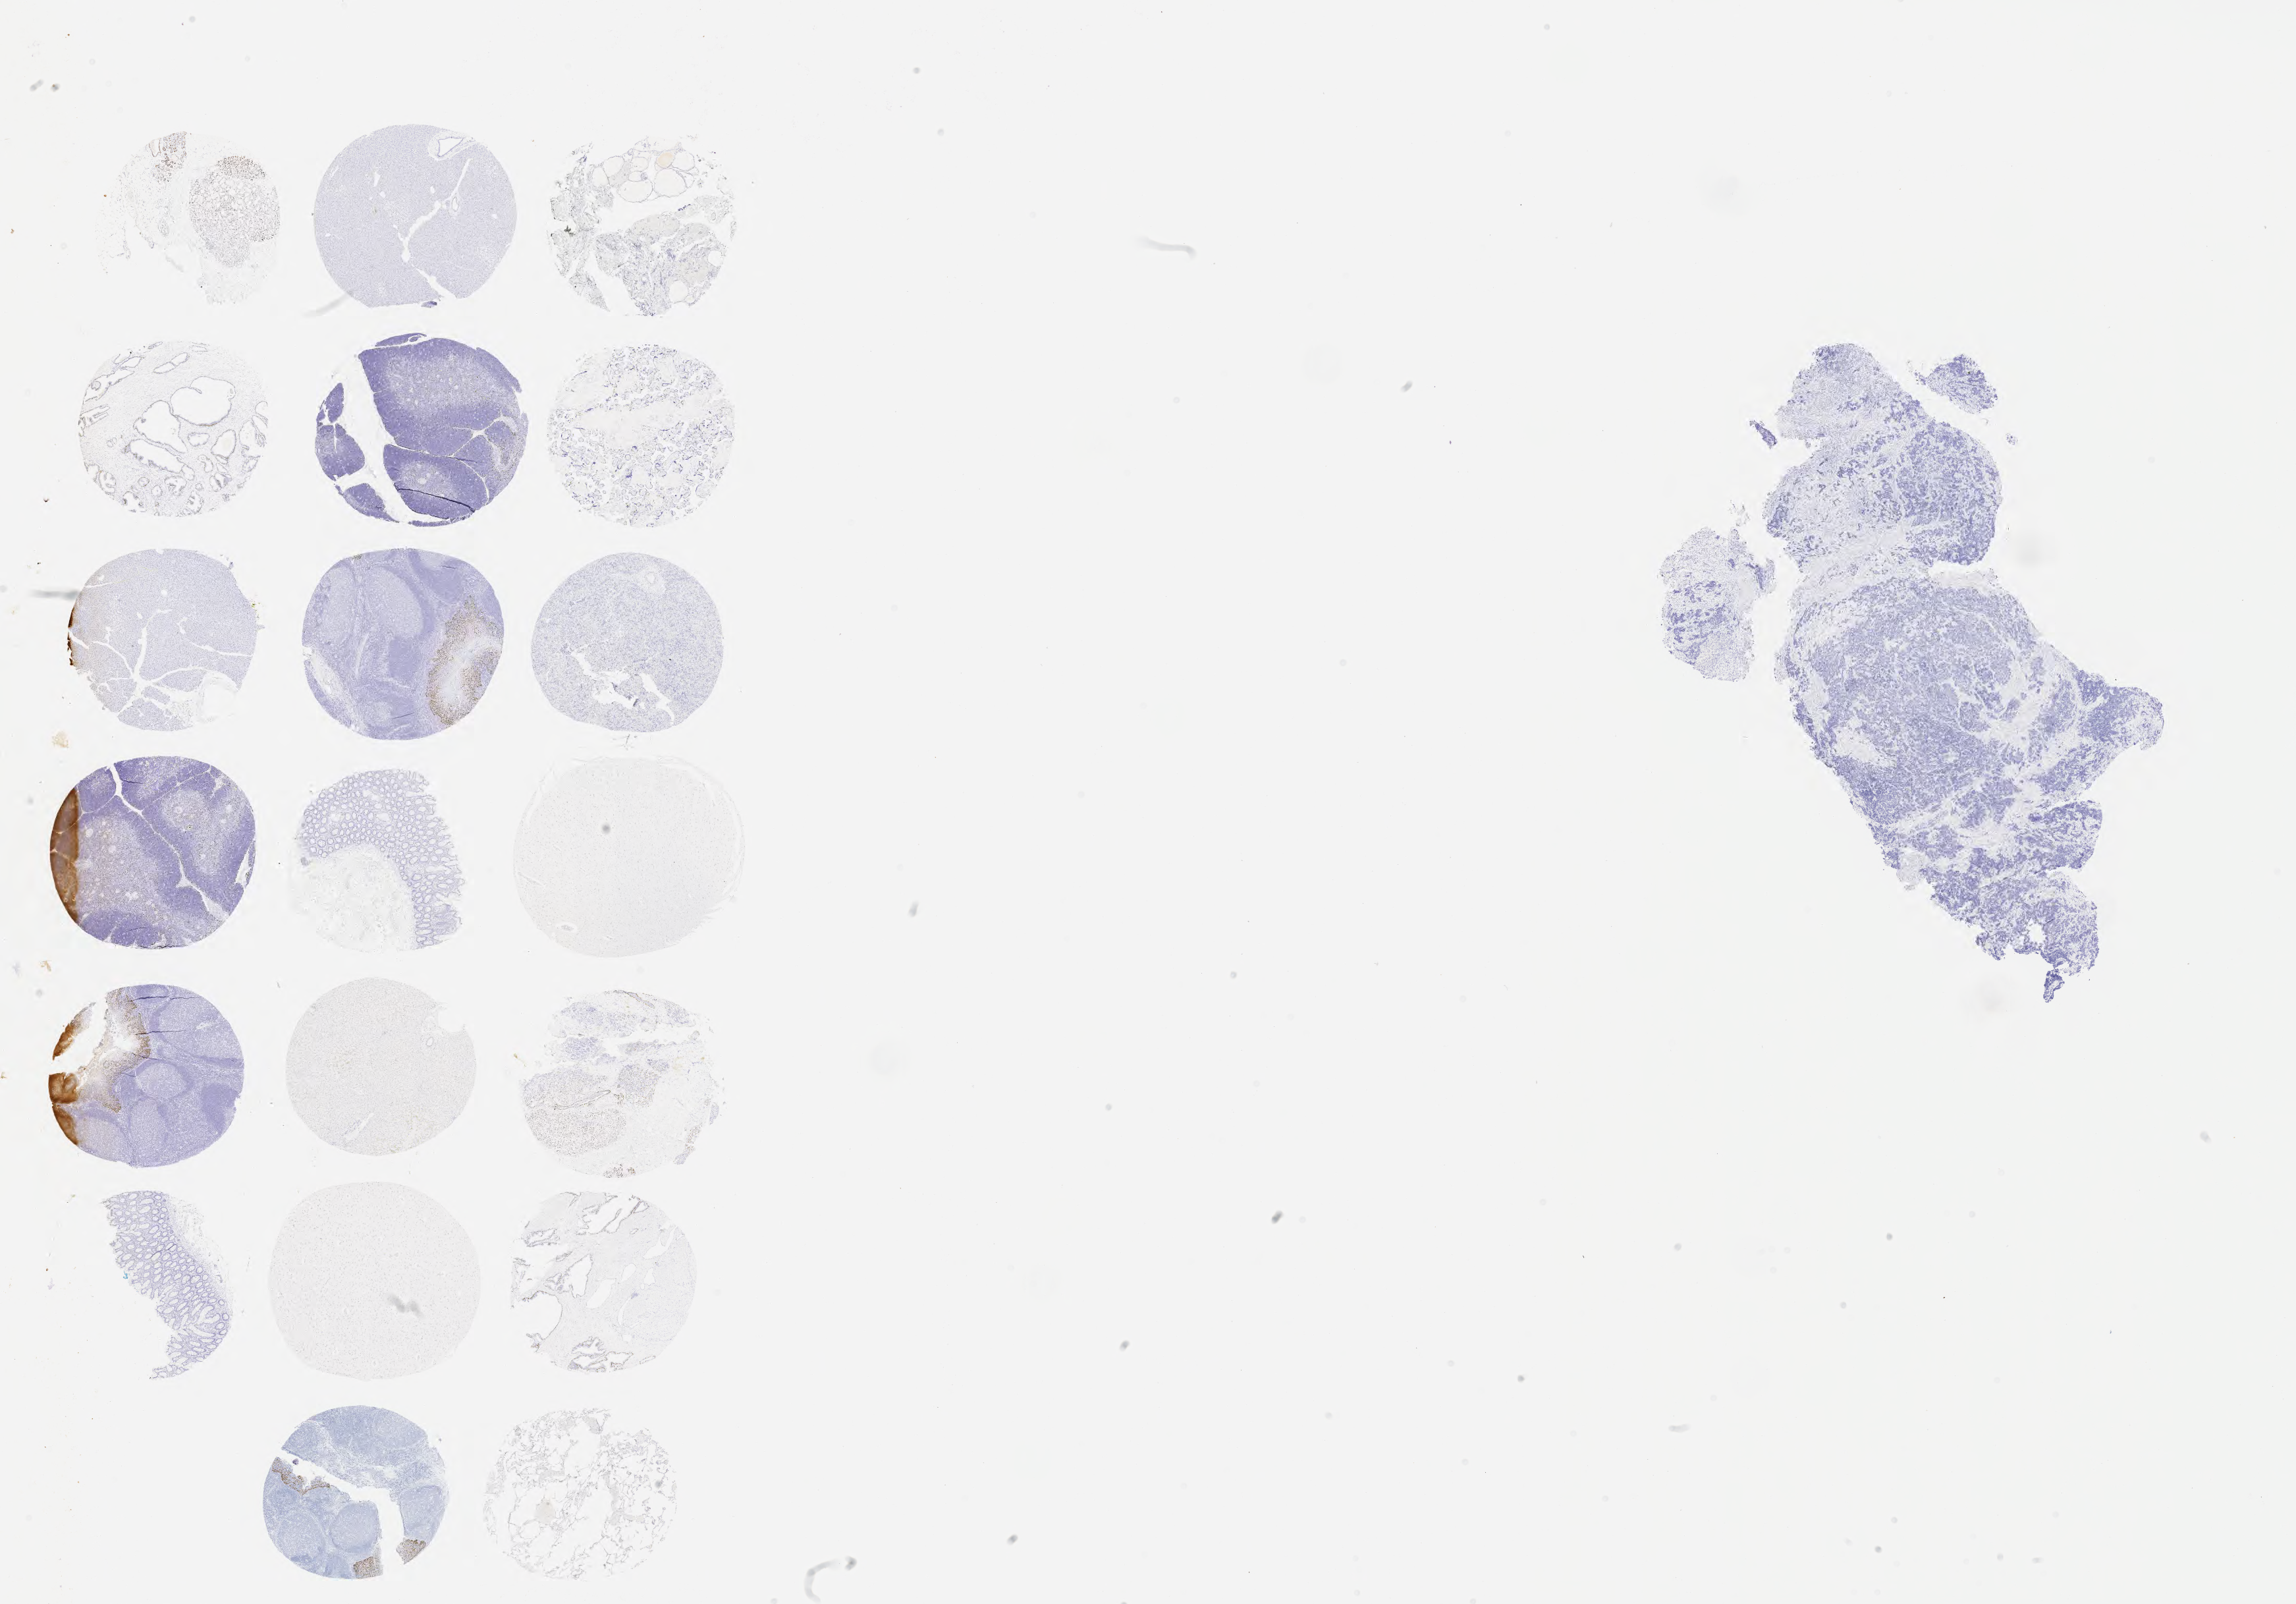
Immunohistochemistry (IHC) whole-slide image stained for p40, whole scanned area (about 28.2 x 19.7 mm) shown as a low-resolution overview. Tumor tissue. Site: cervix. Patient female; age 43 years.
Histologic diagnosis: Lymphoepithelial carcinoma.